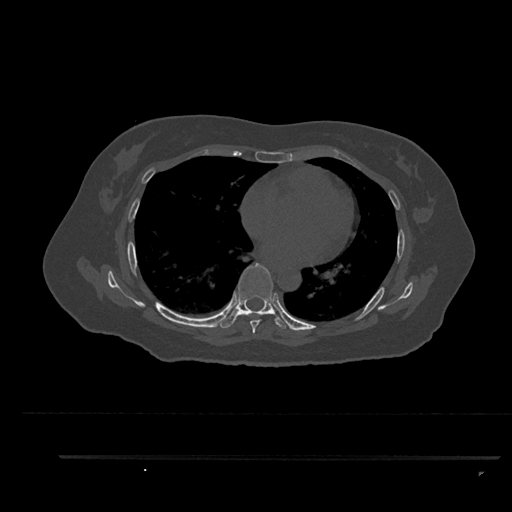
CT including the spine, one axial slice; slice 528 of 797 in the series (ordered by position); bone window (W 1800 / L 400 HU); 0.5 mm slice thickness; 512 × 512 image matrix, field of view 408 × 408 mm. Patient: female, 44 years. Case-level facts recorded for this patient, not image findings: primary cancer: renal.
Structures marked on this image (semi-automatic segmentation, software-assisted and operator-edited):
- T6 vertebra: bounding box <250,315,261,334> (left, top, right, bottom; pixels)
- T7 vertebra: <216,263,289,329>